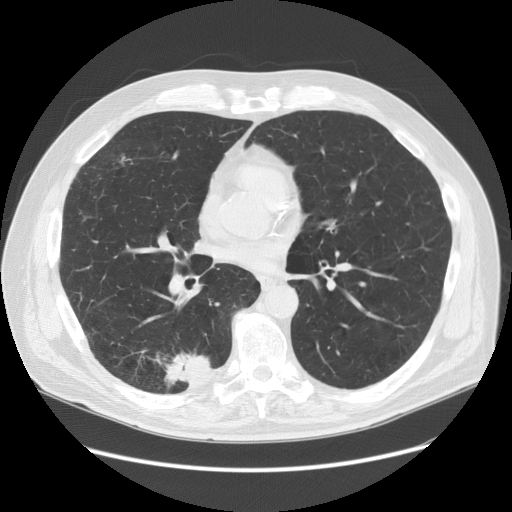
Low-dose screening chest CT, one axial slice. Slice 71 of 149 in the series (ordered by position). Reconstruction kernel STANDARD. 120 kVp. Lung window (W 1500 / L -600 HU). 2.5 mm slice thickness. 512 × 512 image matrix, field of view 400 × 400 mm.
Structures marked on this image (expert manual segmentation):
- lesion 1 (tumor, lower lobe of right lung): bounding box (x1, y1, x2, y2) in pixels: (165, 353, 217, 386)